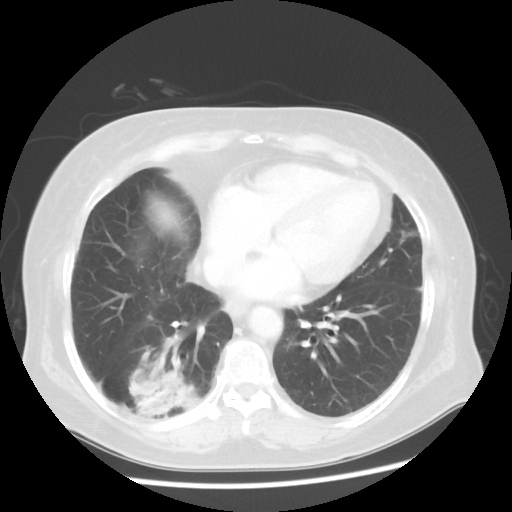
Chest CT, one axial slice; slice 21 of 56 in the series (ordered by position); reconstruction kernel STANDARD; lung window (W 1500 / L -600 HU); 5 mm slice thickness; 512 × 512 image matrix, field of view 360 × 360 mm. Patient: female, 64 years. From the clinical record (not read from this slice): clinical TNM (as recorded): Tis N0 M0.
Annotated regions visible in this slice (bounding box drawn by a radiologist):
- lung tumour (recorded histology: adenocarcinoma): box from (x=125, y=351) to (x=210, y=433) px